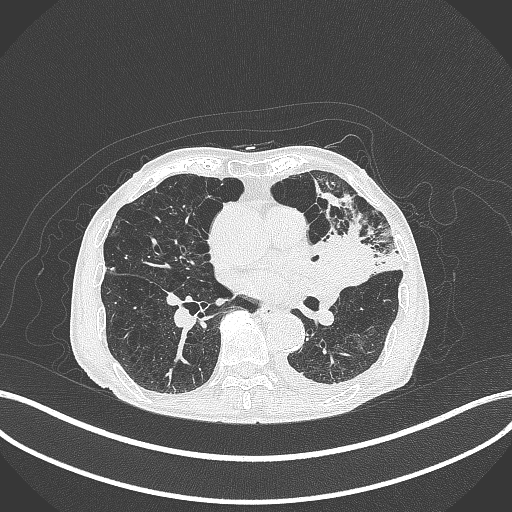
Chest CT, one axial slice. Slice 182 of 385 in the series (ordered by position). 120 kVp. Lung window (W 1500 / L -600 HU). 512 × 512 image matrix, field of view 400 × 400 mm. Male patient, age 90 years or older. From the clinical record (not read from this slice): clinical TNM (as recorded): T2b N1 M0.
Structures marked on this image (rectangle marked by the reading radiologist):
- lung tumour (recorded histology: squamous cell carcinoma): bounding box <319,231,375,290> (left, top, right, bottom; pixels)